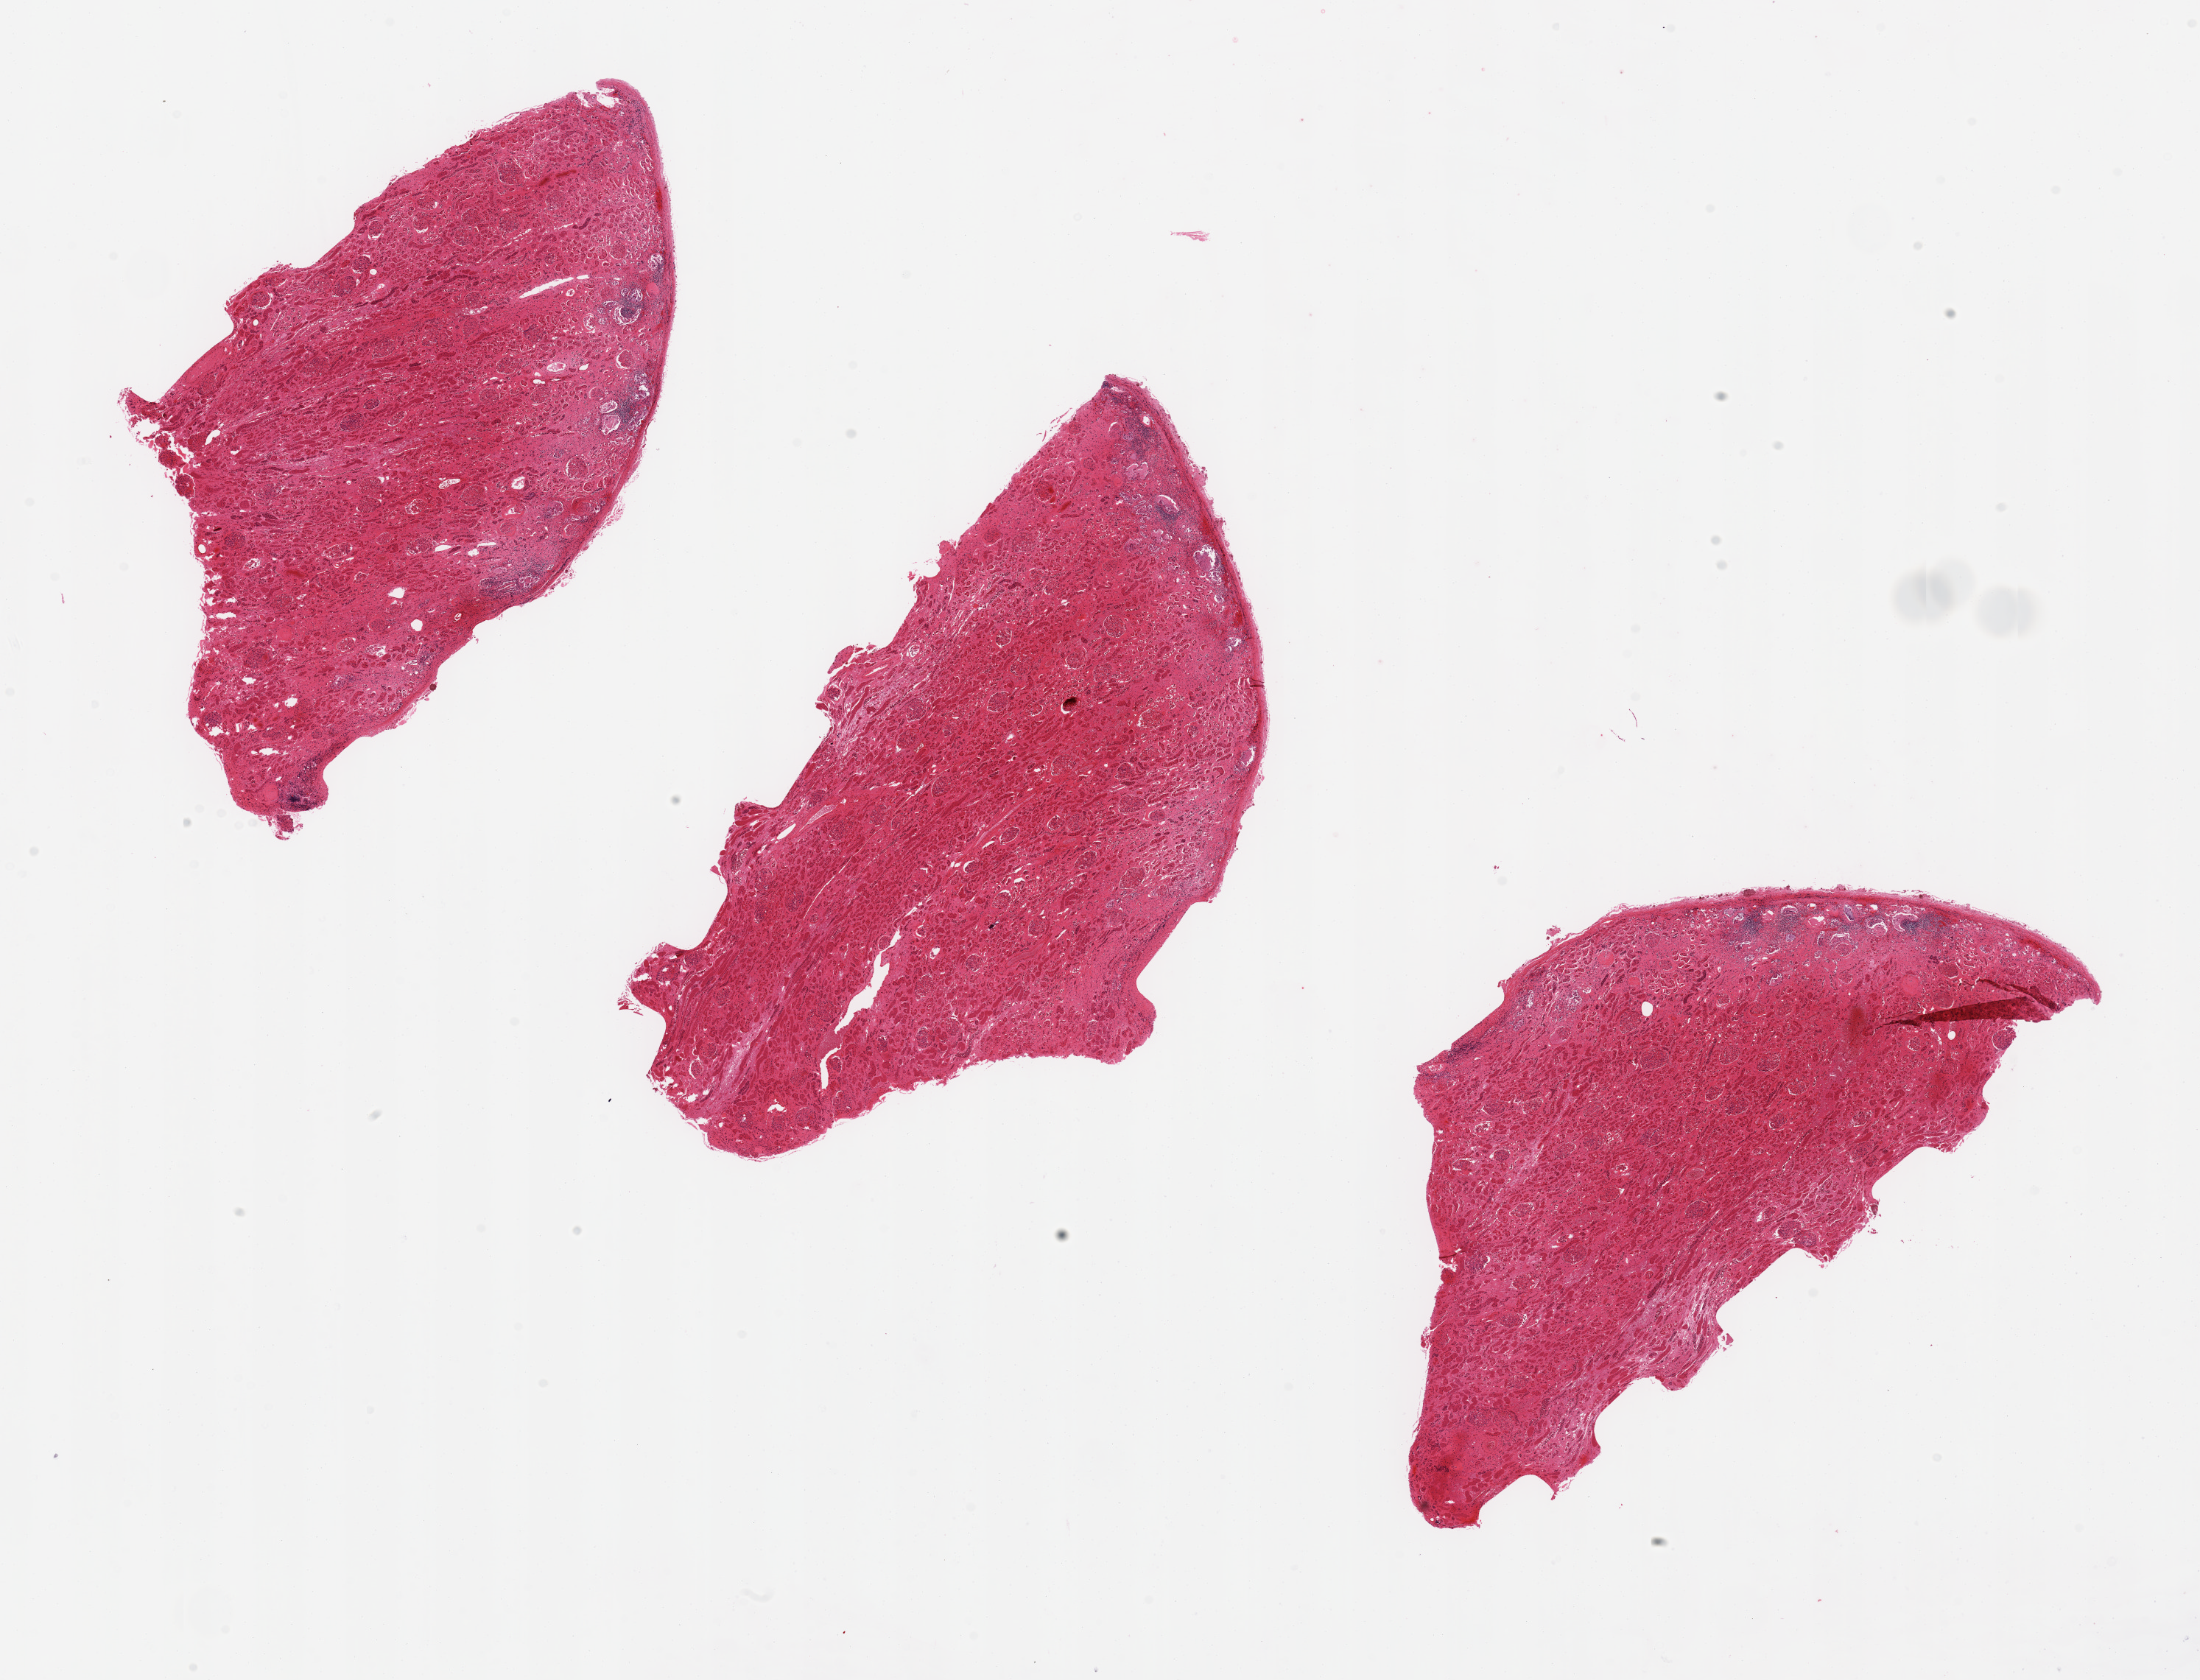
Whole-slide image, hematoxylin and eosin (H&E) stain, whole scanned area (about 23.6 x 18.0 mm, acquisition: 20x scan) shown as a low-resolution overview. PAXgene-fixed paraffin-embedded (PFPE) section. Section of renal cortex (target tissue). Tissue donor sample. Donor: male.
Reviewer comment on this tissue sample: 3 pieces 9x4 mm. Interstitial fibrosis, glomerular thickening, moderate tubular autolysis.